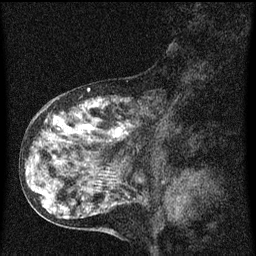
Breast MRI (dynamic contrast-enhanced), one sagittal slice; slice 26 of 60 in the series (ordered by position); dynamic contrast-enhanced series, image 2 of 3 at this slice position (ordered by acquisition); 1.5 T; TE 4.2 ms, TR 8 ms; 2 mm slice thickness; 256 × 256 image matrix, field of view 180 × 180 mm. Patient: female, 55 years.
Annotated regions visible in this slice (semi-automatically segmented with operator editing):
- analysis volume of interest (the breast-tissue region the enhancement analysis was run in; not a lesion): bounding box [x1, y1, x2, y2] px = [38, 92, 161, 159]
- tumour enhancement mask (voxels above the 70 % enhancement threshold inside the analysis volume of interest): [46, 116, 133, 139]